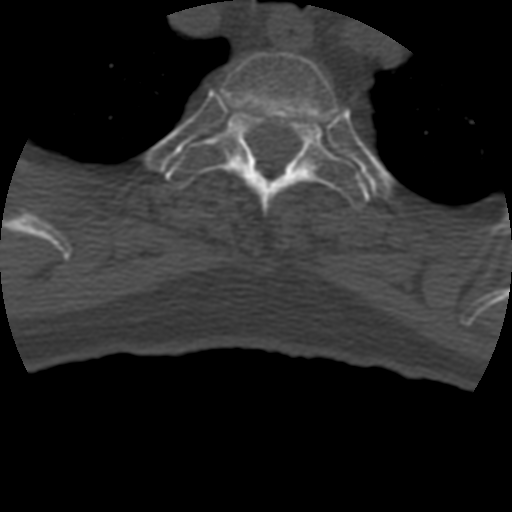
CT including the spine, one axial slice; position 358 of 399 along the scan axis; 120 kVp; bone window (W 1800 / L 400 HU); 1.25 mm slice thickness; 512 × 512 image matrix, field of view 160 × 160 mm. Patient age 69 years. From the clinical record (not read from this slice): primary cancer: prostate.
Annotated regions visible in this slice (semi-automatically segmented with operator editing):
- T2 vertebra: bounding box <220,52,343,123> (left, top, right, bottom; pixels)
- T3 vertebra: <165,110,370,217>